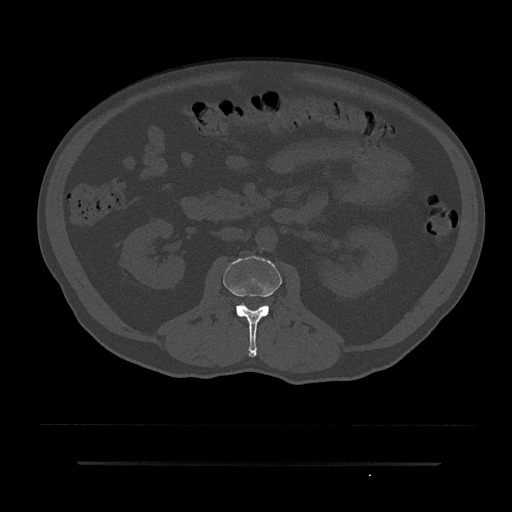
CT including the spine, one axial slice. Position 62 of 797 along the scan axis. Reconstruction kernel Br40s/3. 120 kVp. Bone window (W 1800 / L 400 HU). 0.5 mm slice thickness. 512 × 512 image matrix, field of view 464 × 464 mm. Male patient, age 59 years. From the clinical record (not read from this slice): primary cancer: bile ducts.
Outlined on this slice (semi-automatically segmented with operator editing):
- L2 vertebra: bounding box [x1, y1, x2, y2] px = [223, 256, 282, 357]